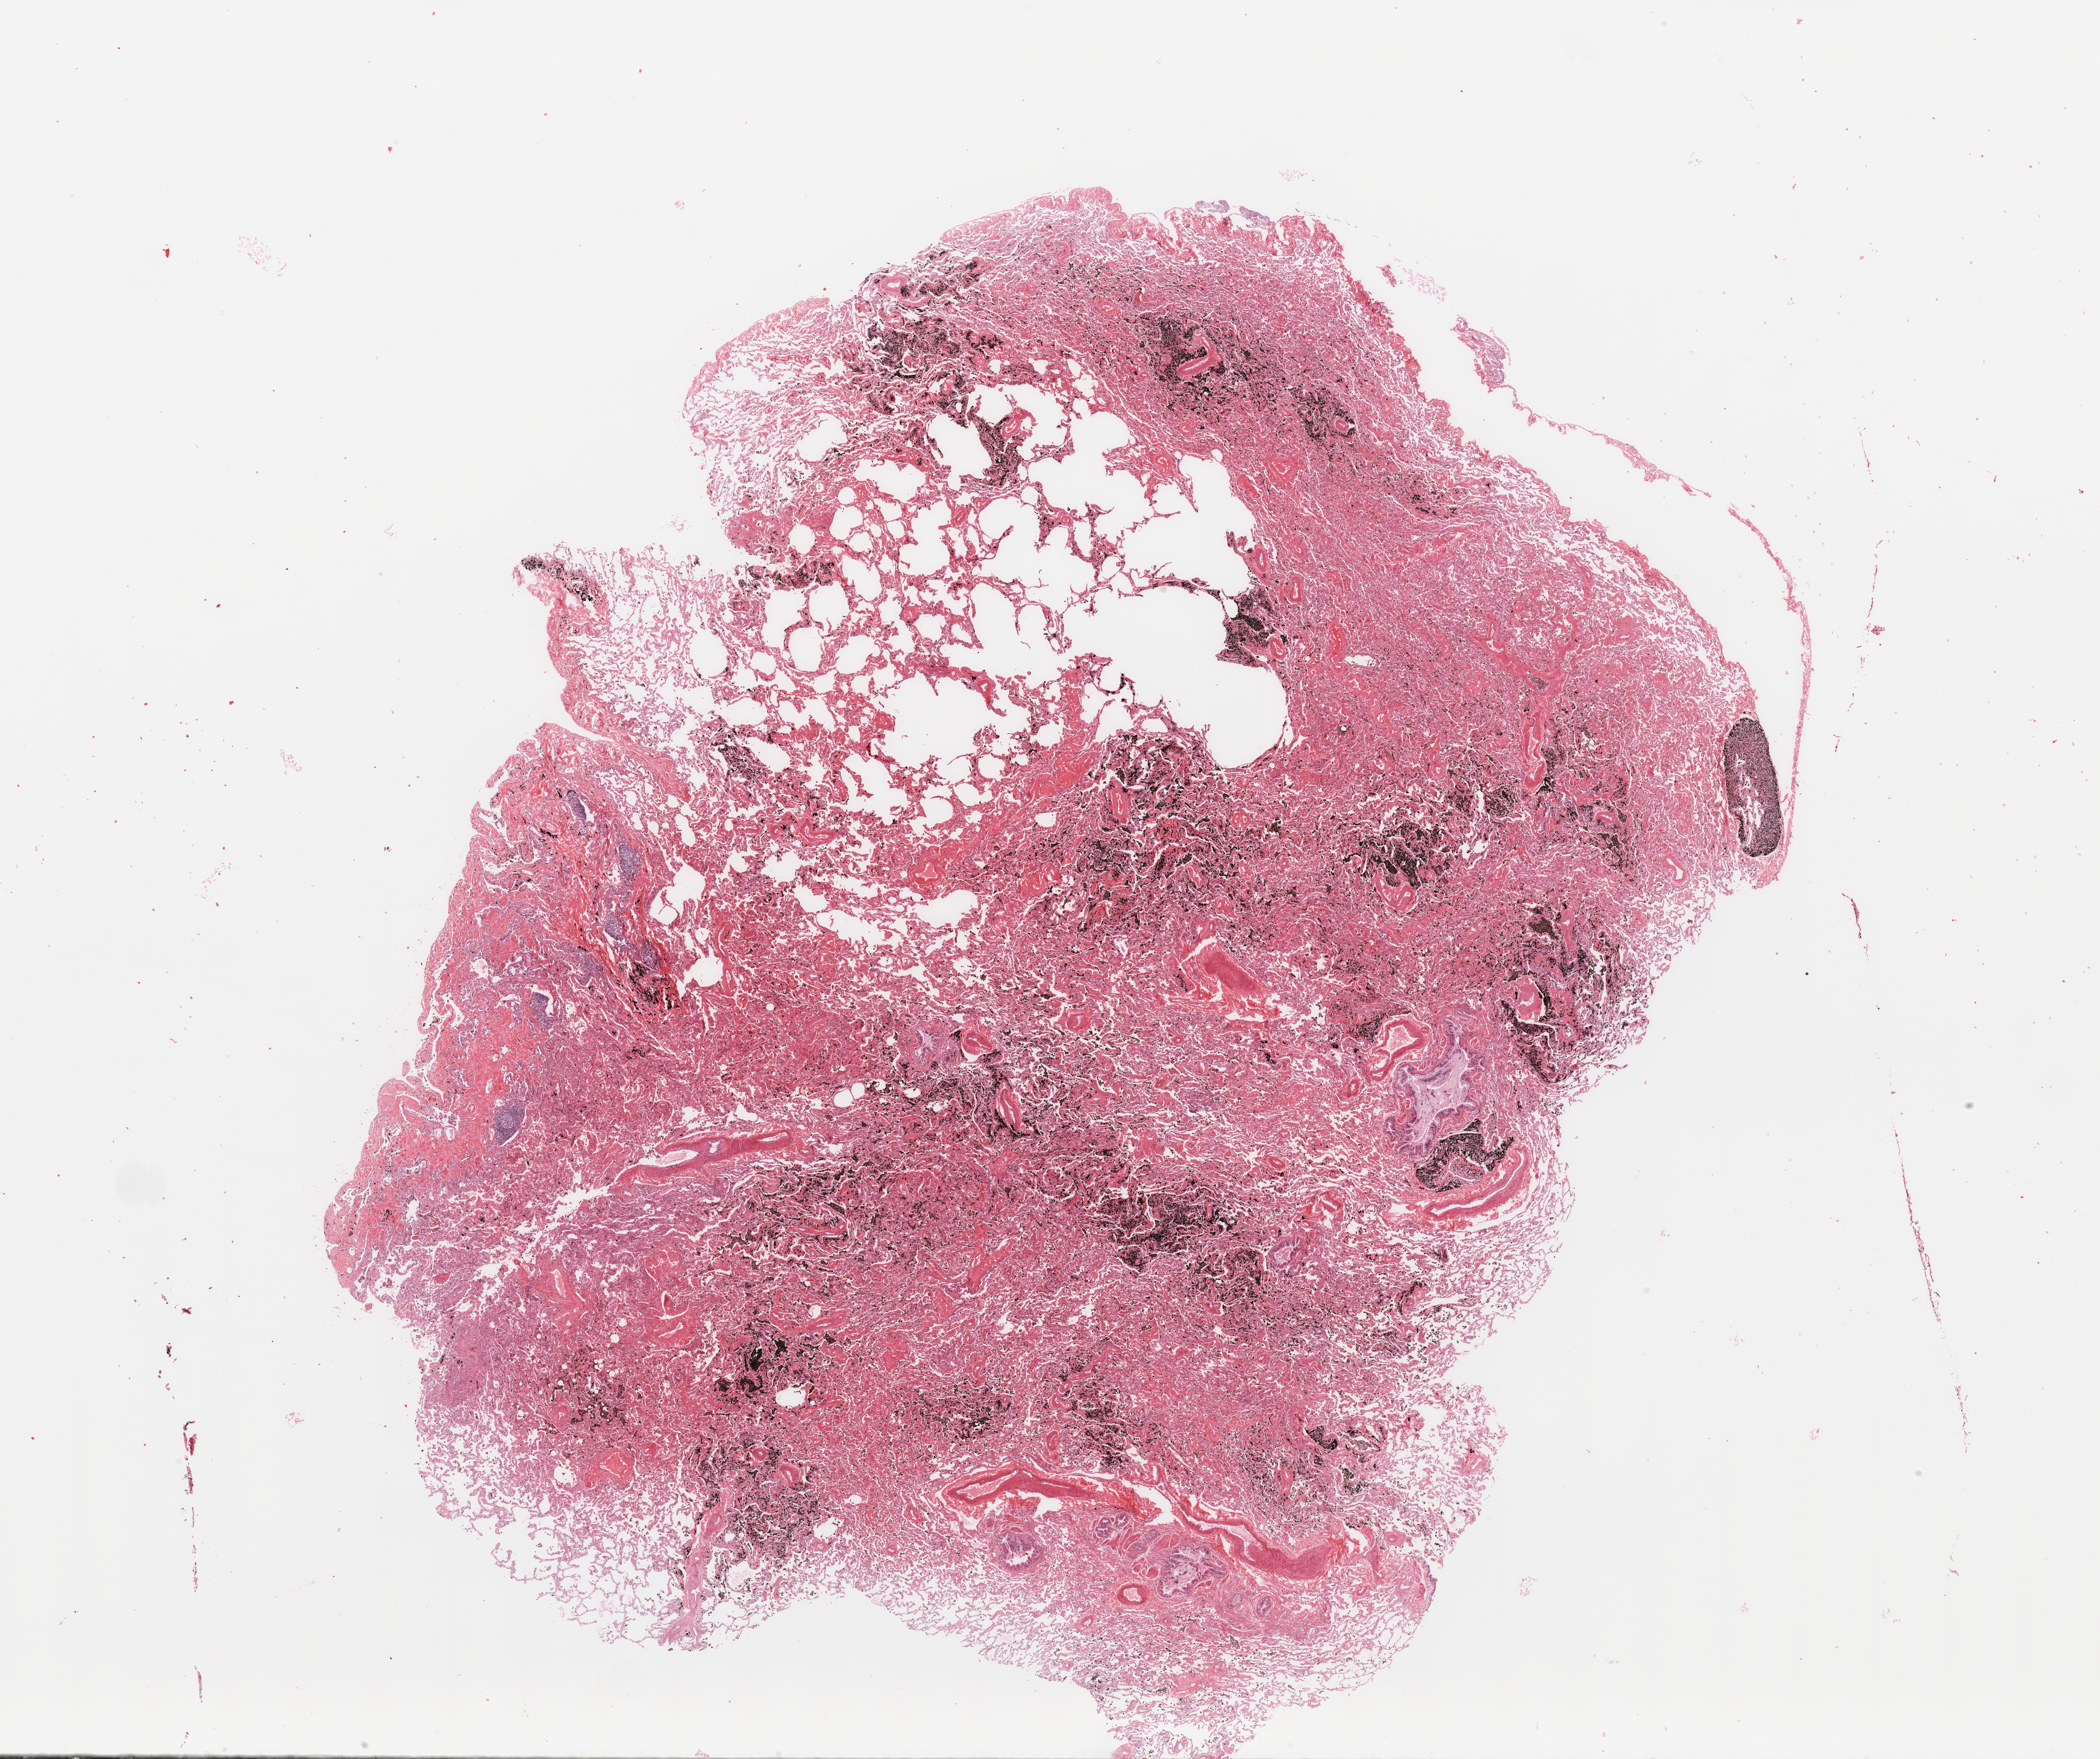
Digitized H&E tissue section (whole slide) — a low-resolution overview of the entire scanned area, about 27.6 x 23.1 mm (from a 20x scan), lung, normal (non-tumour) tissue. 65-year-old male patient.
This section: normal (non-tumour) tissue from the same patient. Patient diagnosis: Squamous cell carcinoma, NOS.